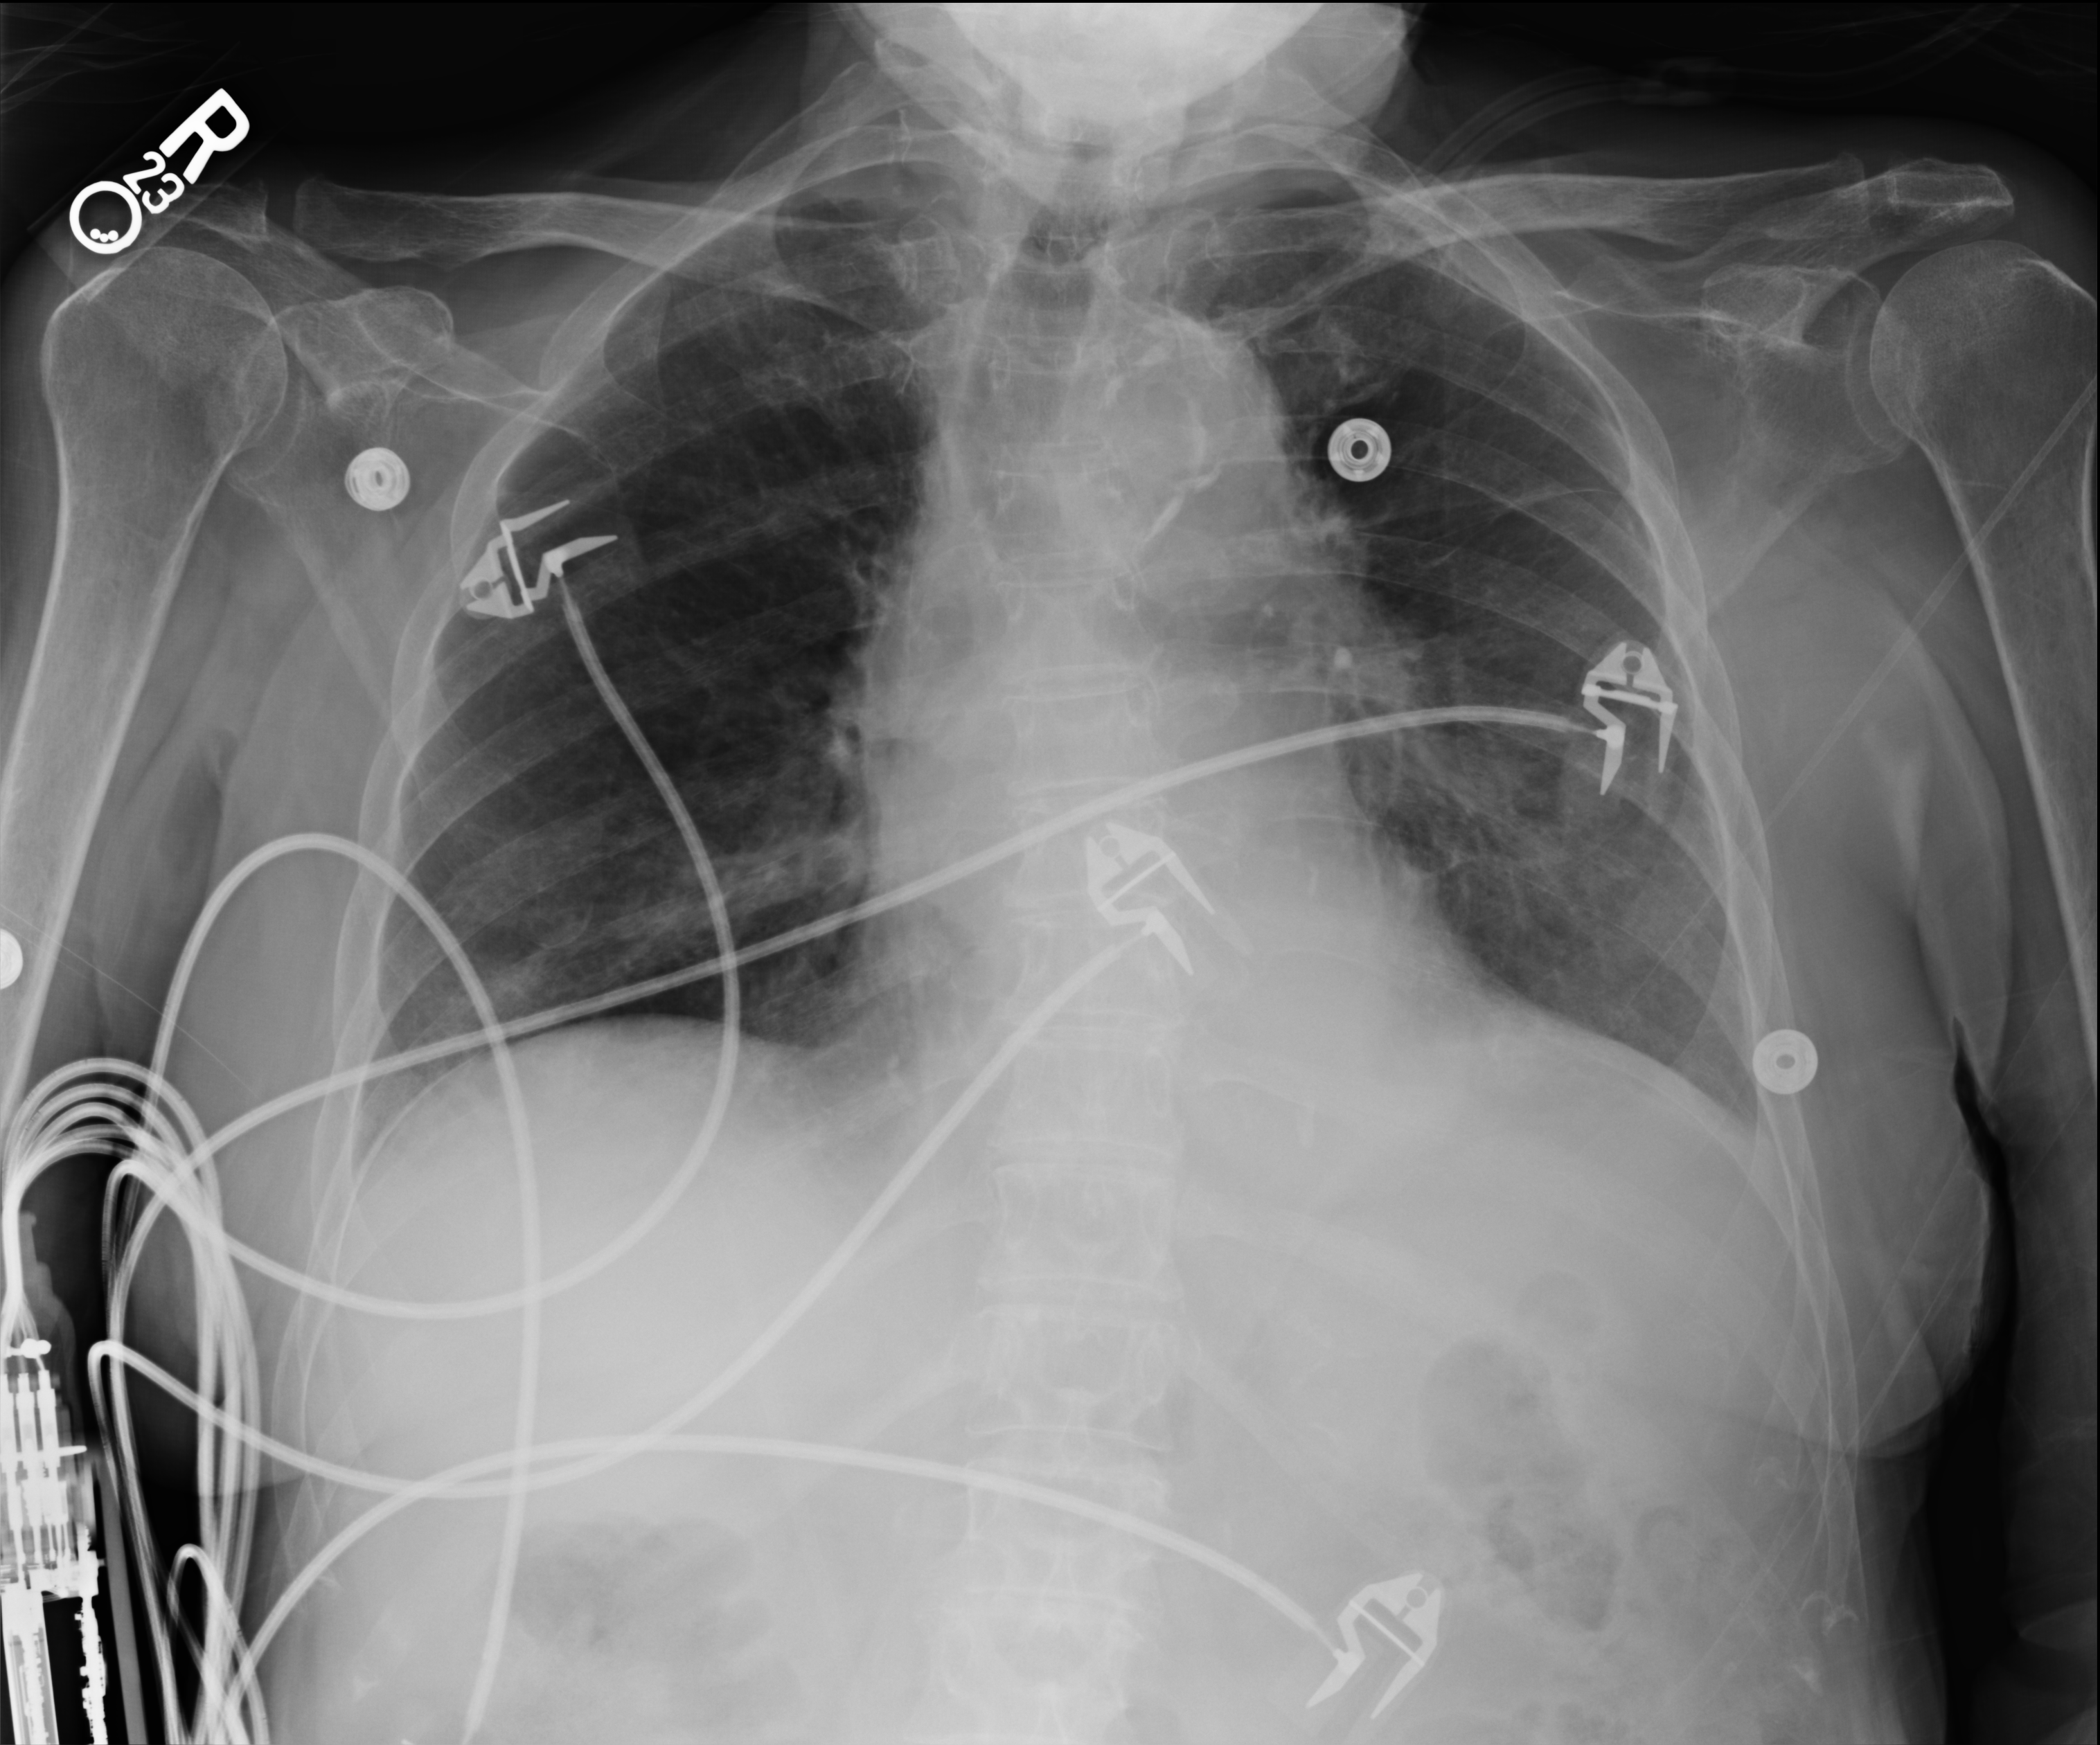
Portable chest radiograph, anteroposterior (AP) projection. Female patient hospitalised with COVID-19, age 75–90 years.
Hospital-stay facts (about this admission, not read from this image; timing relative to this image not recorded): COPD (admission record): no; mechanically ventilated during this hospital stay: no.